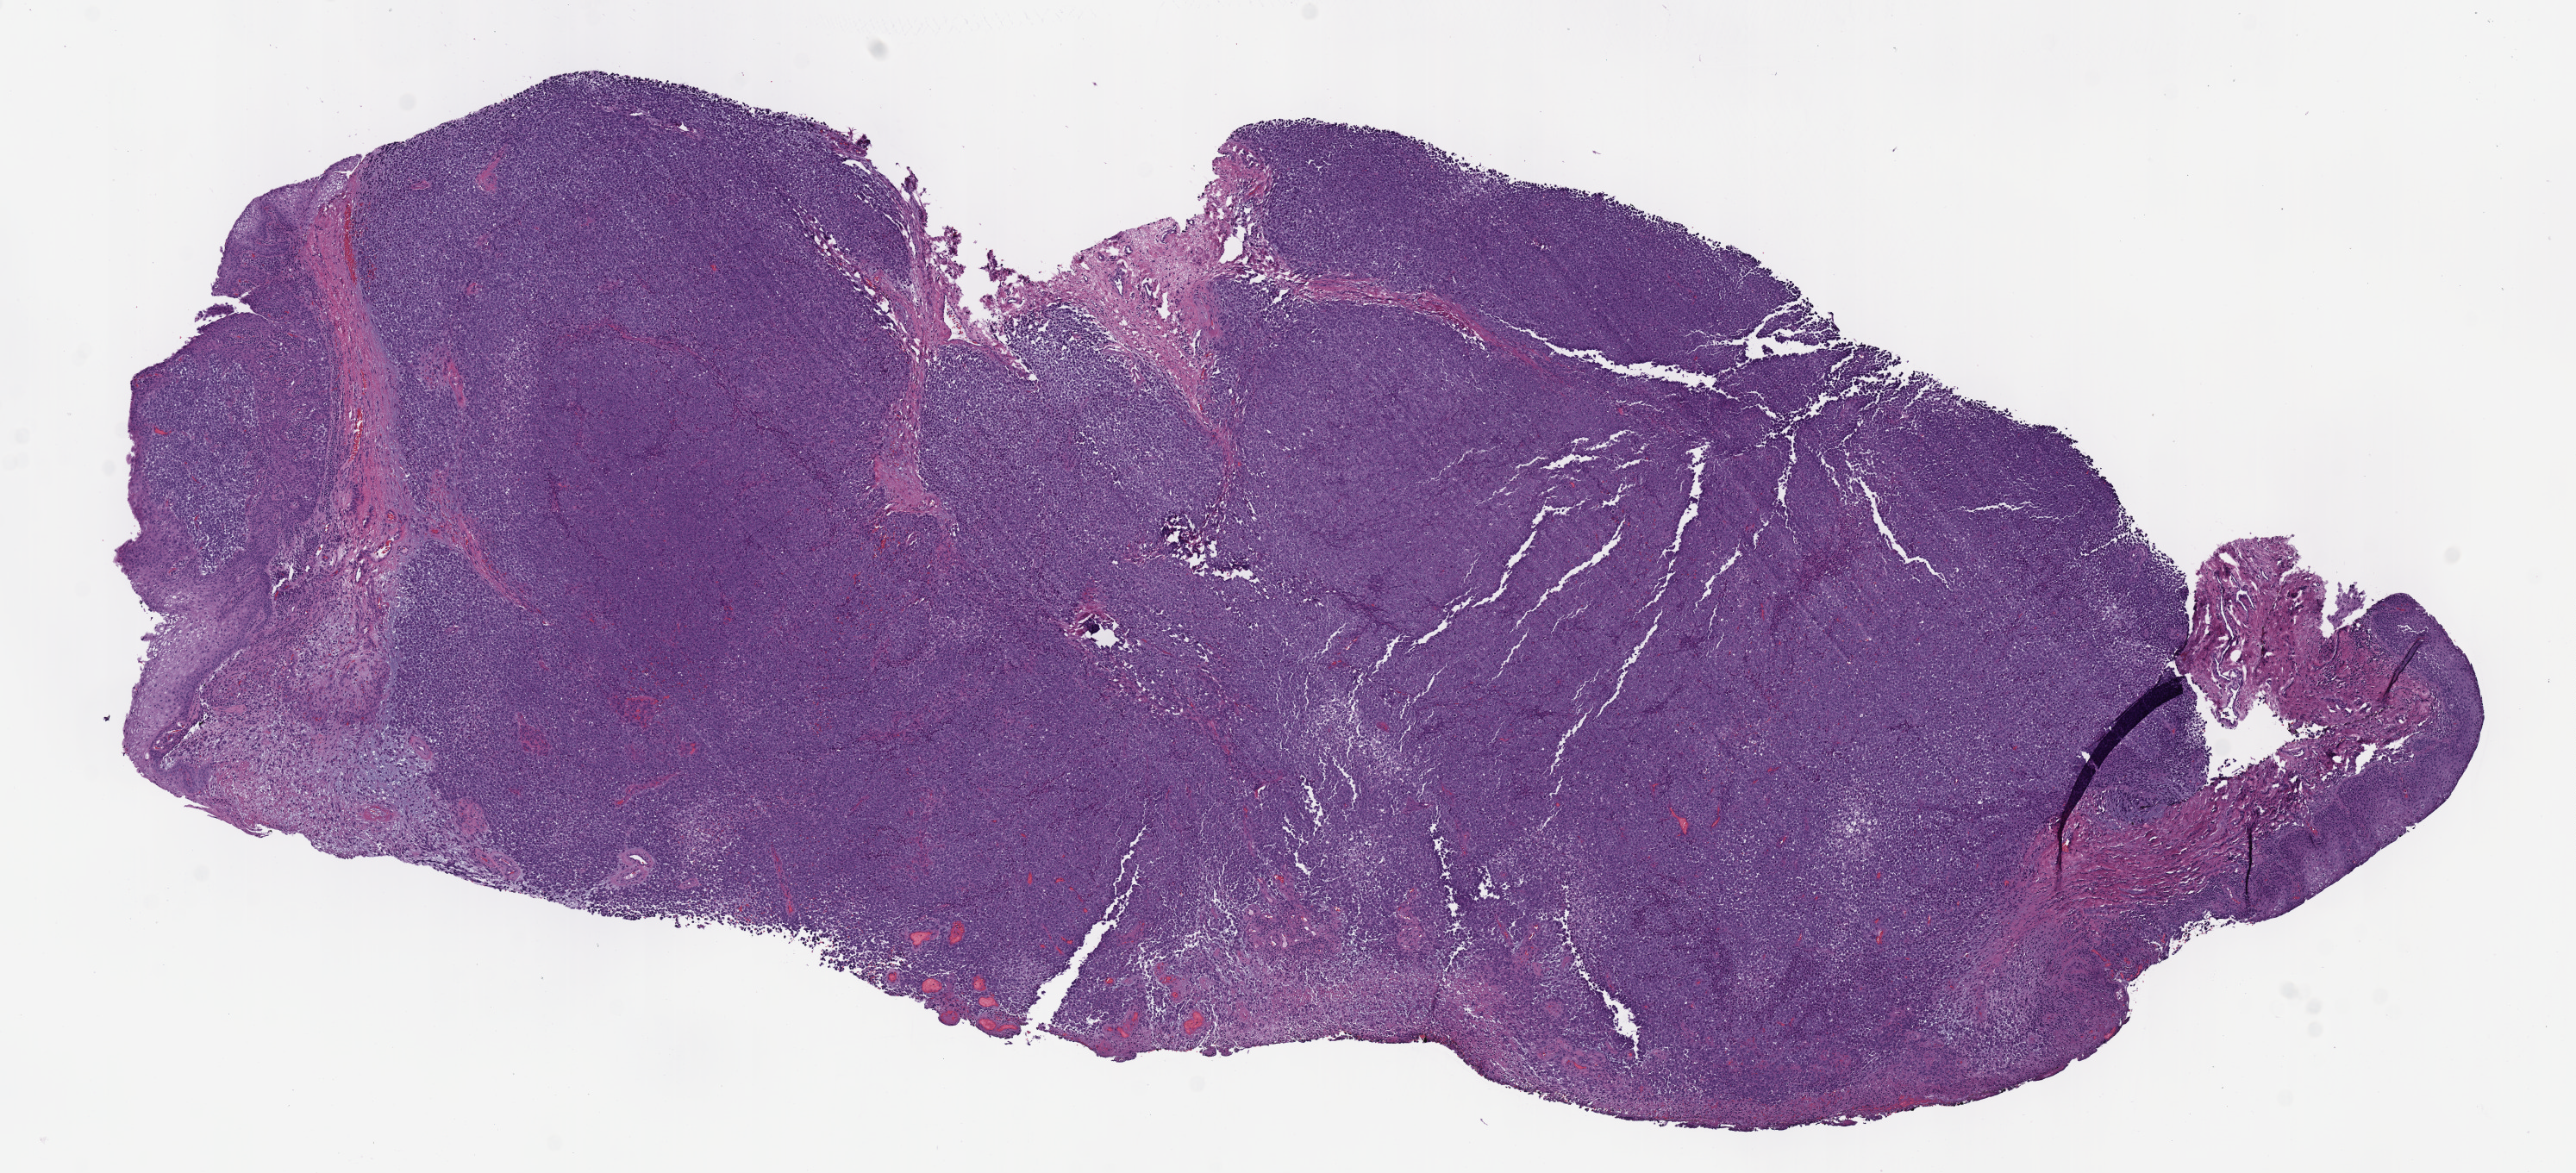
Whole-slide histology image, H&E-stained — shown as a low-resolution overview of the whole scanned area (about 11.7 x 5.4 mm); FFPE section; metastatic tumour sample, sampled site: vagina. Female patient; age at initial diagnosis 59 years.
This section: metastatic tumour tissue. Patient diagnosis: Malignant melanoma, NOS.